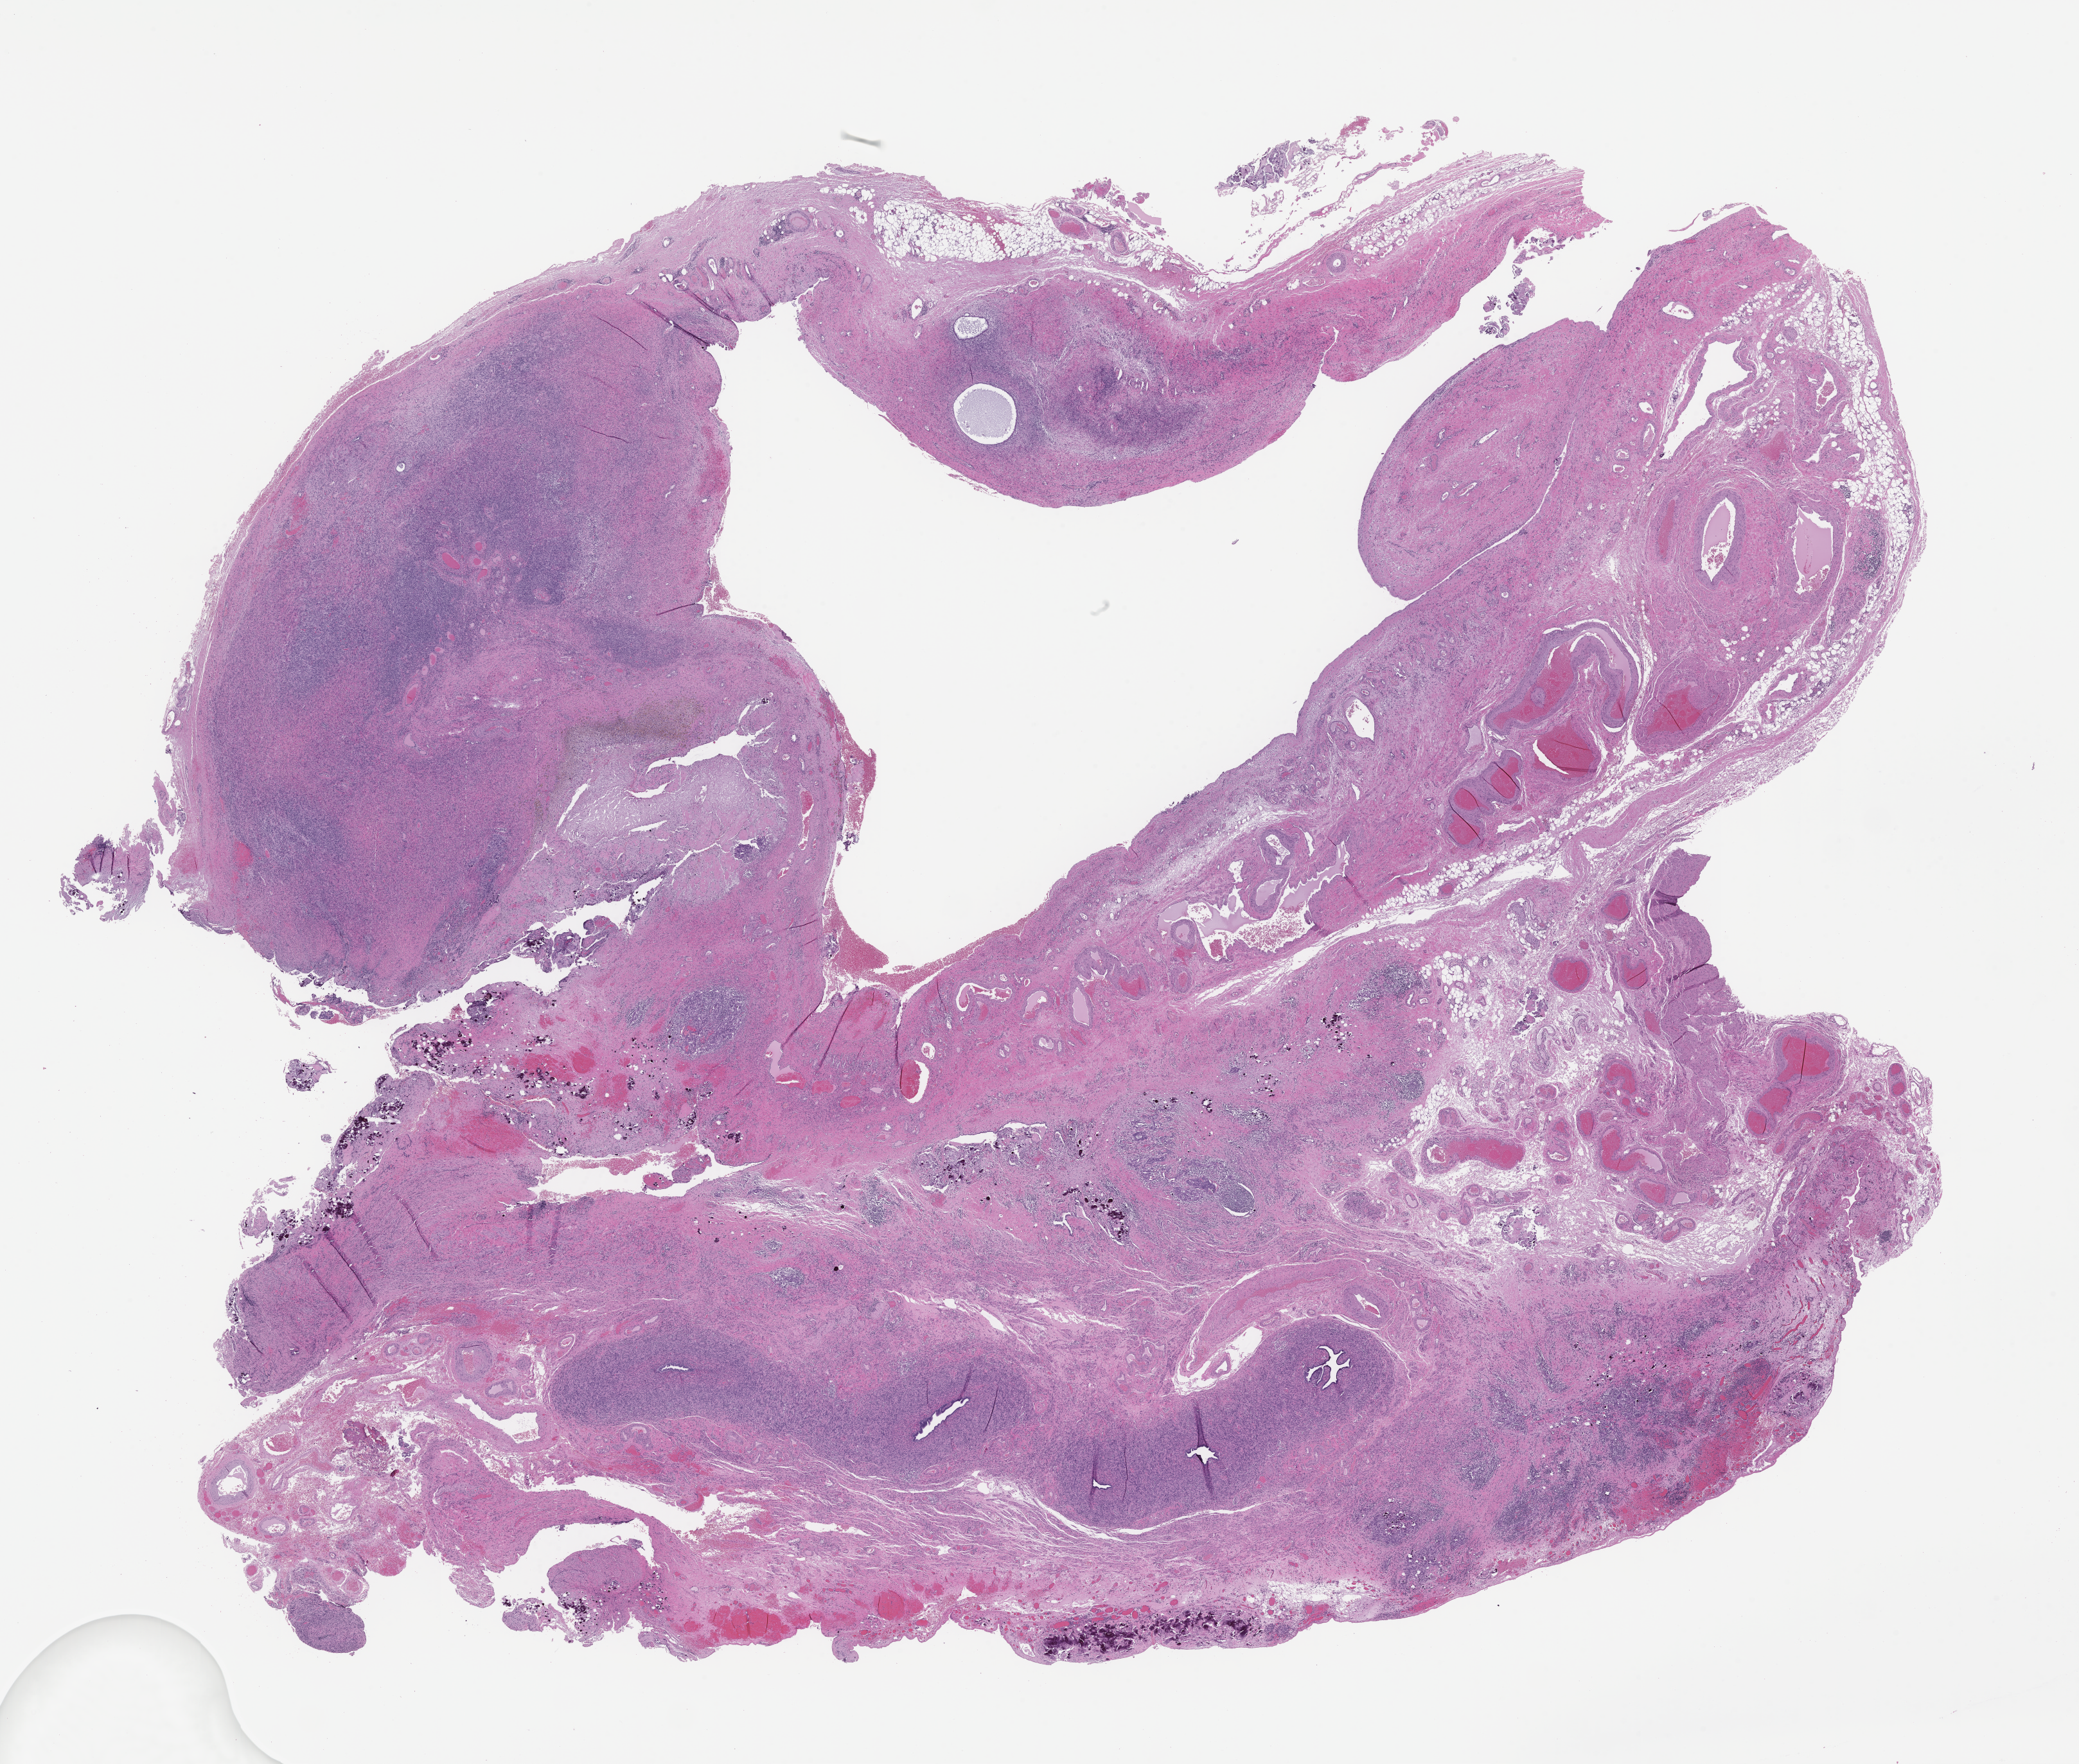
Whole-slide image, H&E stain — a low-resolution overview of the entire scanned area, about 26.1 x 22.2 mm, formalin-fixed, paraffin-embedded (FFPE) tissue, site: ovary, specimen time point: archival tissue. Patient: female.
This section: primary tumour tissue. Diagnosis: Ovarian Carcinoma.